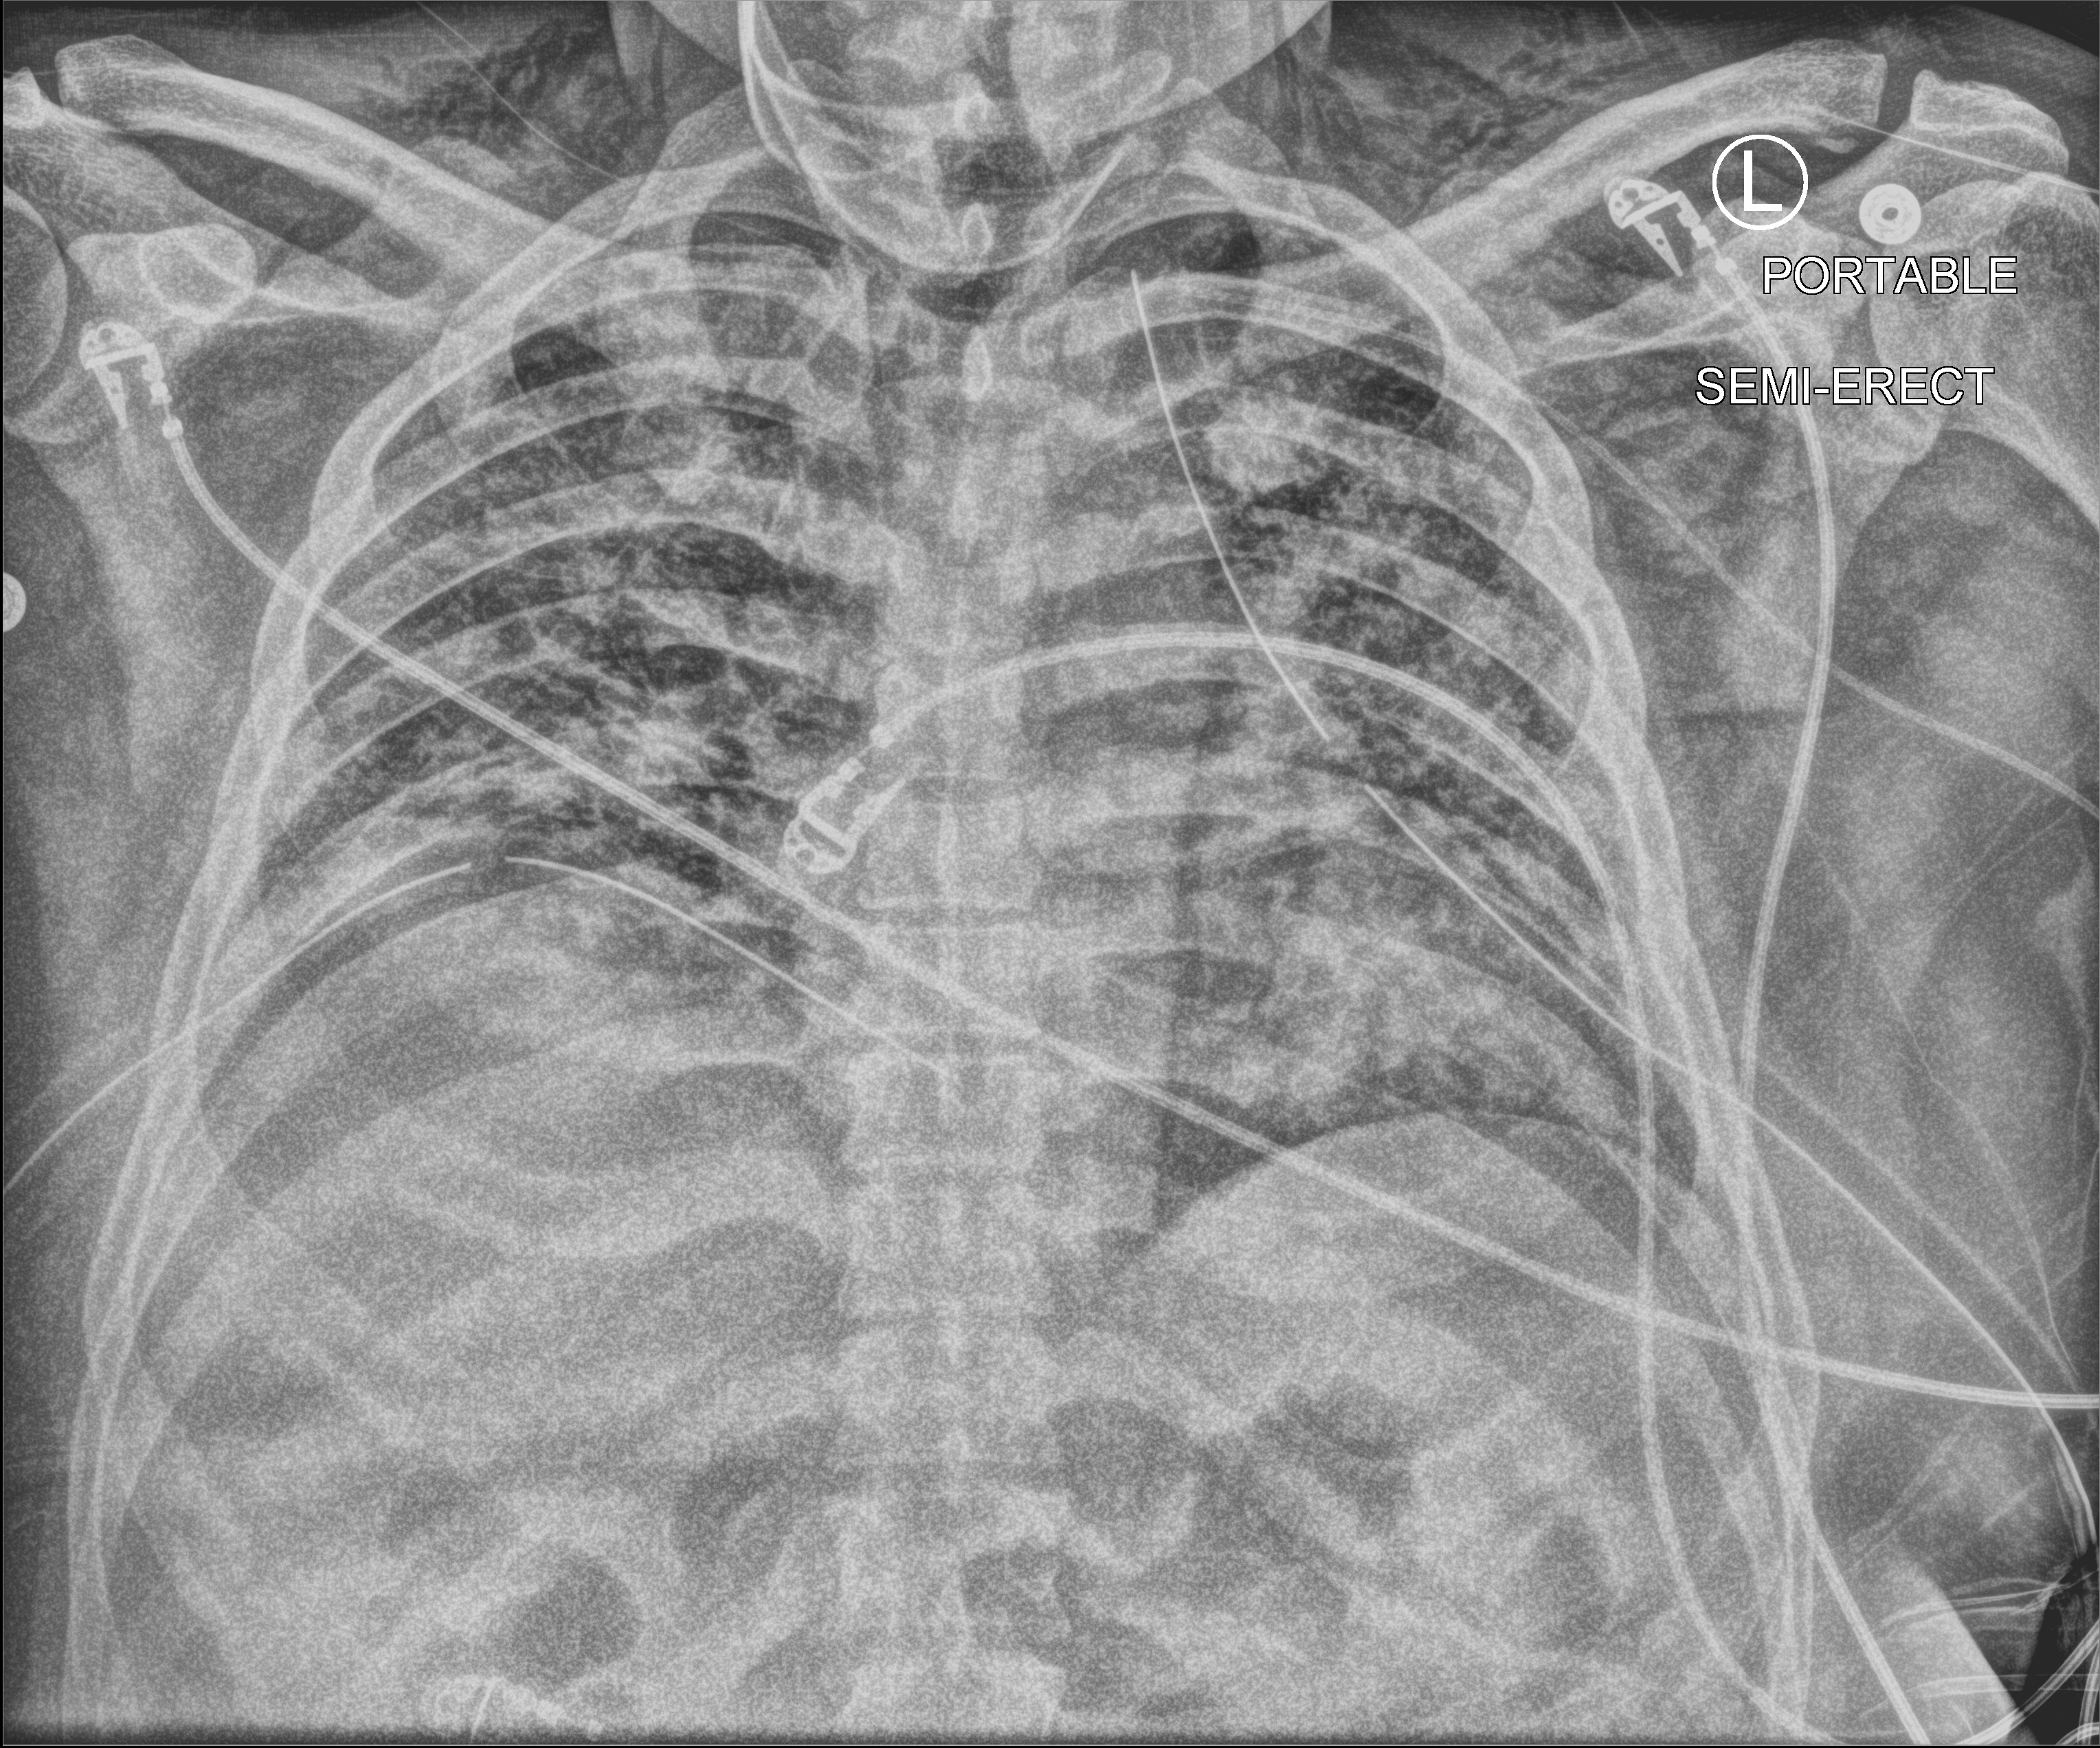
Chest X-ray (portable). Male patient hospitalised with COVID-19, age 18–59 years.
From the hospital-stay record, not from the radiograph (when in the stay this image was taken is not recorded):
- admitted to intensive care during this hospital stay: yes